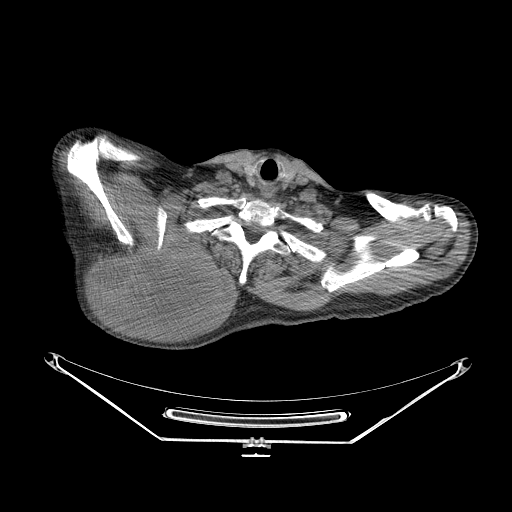
CT of an extremity soft-tissue mass (from a PET/CT study), one axial slice. Position 208 of 267 along the scan axis. Reconstruction kernel STANDARD. 140 kVp. Soft-tissue window (W 400 / L 40 HU). 512 × 512 image matrix, field of view 500 × 500 mm. Male patient. From the clinical record (not read from this slice): histological type: pleiomorphic spindle cell undifferentiated; grade: high; site of the primary tumour: right parascapusular.
Structures marked on this image (expert contour drawn on MRI and transferred to this co-registered scan by the dataset authors):
- gross tumour volume including surrounding oedema: bounding box (x1, y1, x2, y2) in pixels: (89, 235, 232, 328)
- gross tumour volume (mass): (93, 240, 223, 323)